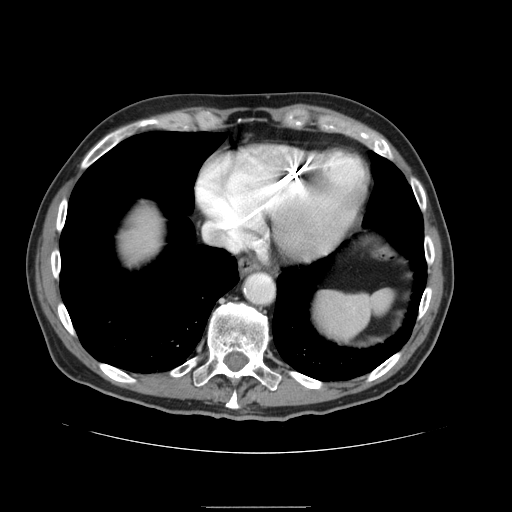
Contrast-enhanced abdominal CT, one axial slice; slice 138 of 168 in the series (ordered by position); 120 kVp; intravenous contrast given; soft-tissue window (W 400 / L 40 HU); 2.5 mm slice thickness; 512 × 512 image matrix, field of view 386 × 386 mm. Male patient, age 74 years. From the clinical record (not read from this slice): diagnosis: colorectal cancer liver metastases, imaged before liver resection; multiple liver metastases: no; largest metastasis: 14.5 cm; disease in both lobes: yes.
Structures marked on this image (outlined manually by an expert reader):
- liver: bounding box <114,201,166,269> (left, top, right, bottom; pixels)
- planned liver remnant (the part of the liver to remain after resection): <114,199,166,268>